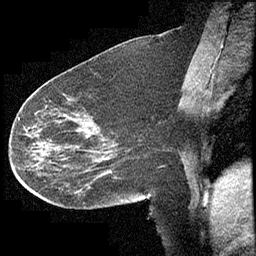
Breast MRI (dynamic contrast-enhanced), one sagittal slice; position 176 of 232 along the scan axis; dynamic contrast-enhanced study with each time point stored as its own series, time point 2 of 4 at this slice position (early post-contrast, ordered by acquisition time); 1.5 T; TE 4.2 ms, TR 6.7 ms; 3 mm slice thickness; 256 × 256 image matrix, field of view 200 × 200 mm. Patient: female, 63 years. From the clinical record (not read from this slice): setting: breast cancer imaged before/during neoadjuvant chemotherapy; receptor status: triple-negative.
Outlined on this slice (semi-automatic segmentation, software-assisted and operator-edited):
- analysis volume of interest (the breast-tissue region the enhancement analysis was run in; not a lesion): bounding box <13,90,140,210> (left, top, right, bottom; pixels)
- tumour enhancement mask (voxels above the 70 % enhancement threshold inside the analysis volume of interest): <19,118,38,151>